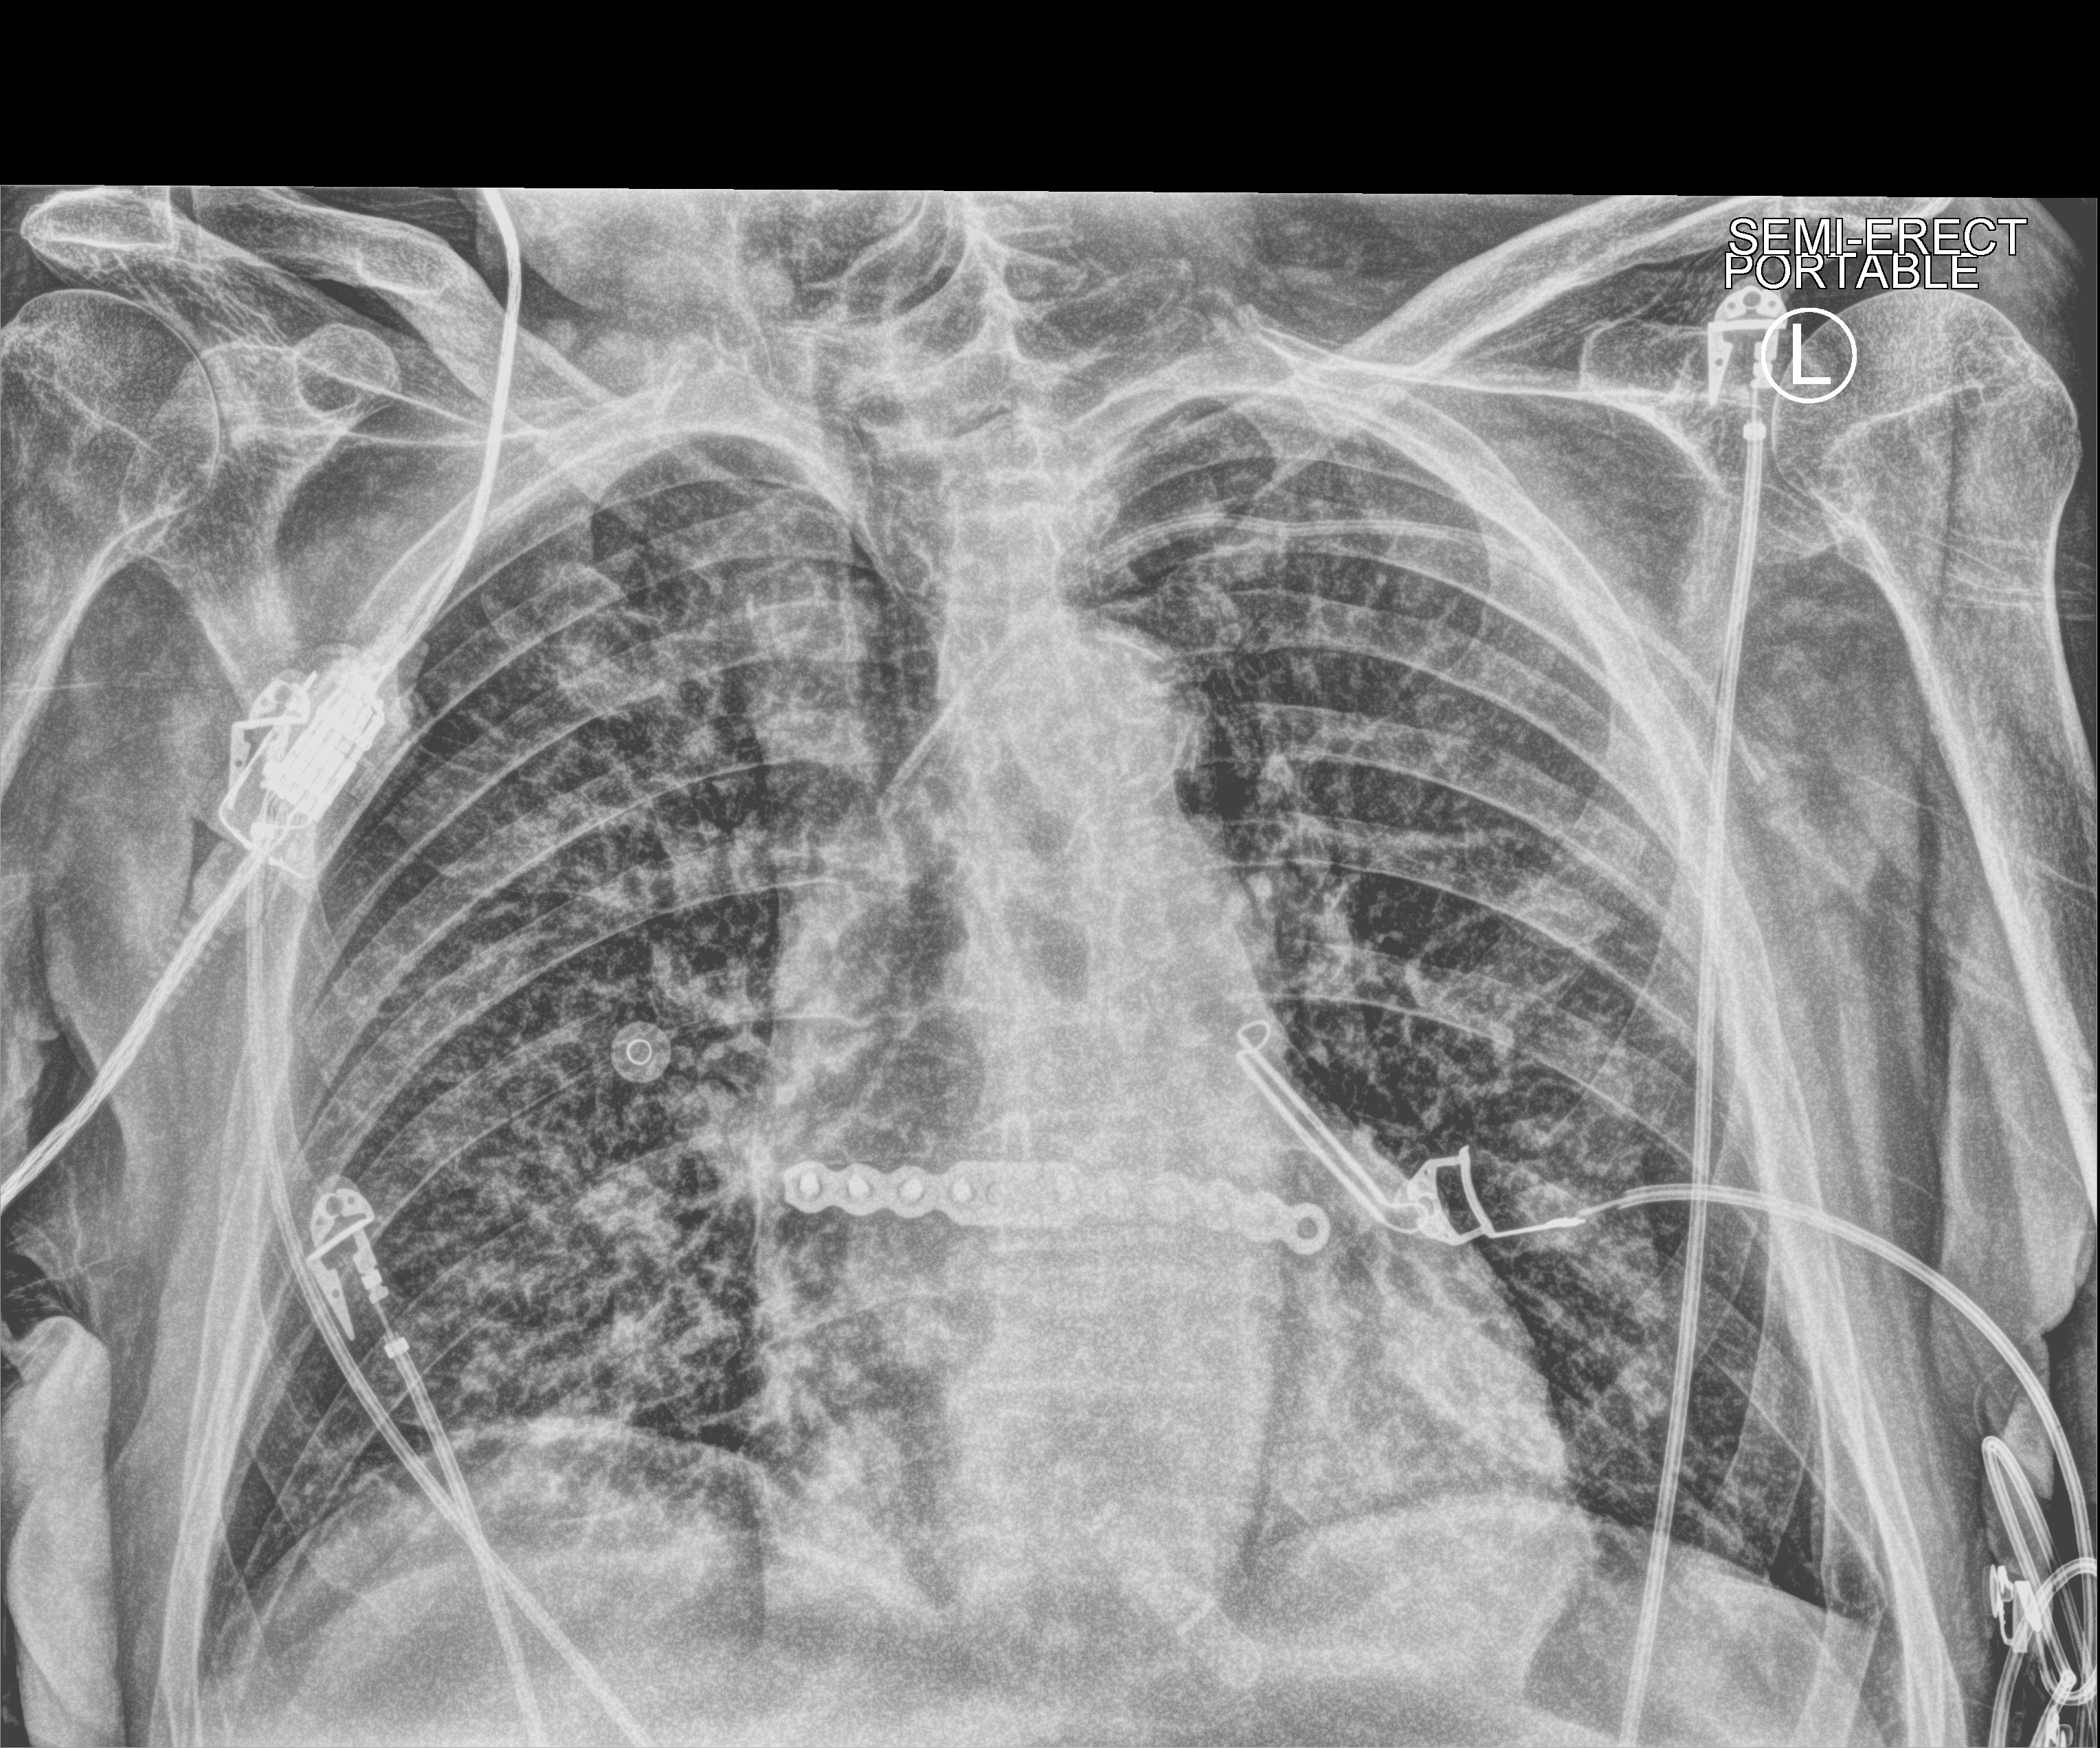
Bedside chest radiograph (computed radiography). Patient hospitalised with COVID-19; male, aged 75–90 years.
From the hospital-stay record, not from the radiograph (when in the stay this image was taken is not recorded):
- other chronic lung disease (admission record): no
- COPD (admission record): yes
- mechanically ventilated during this hospital stay: no